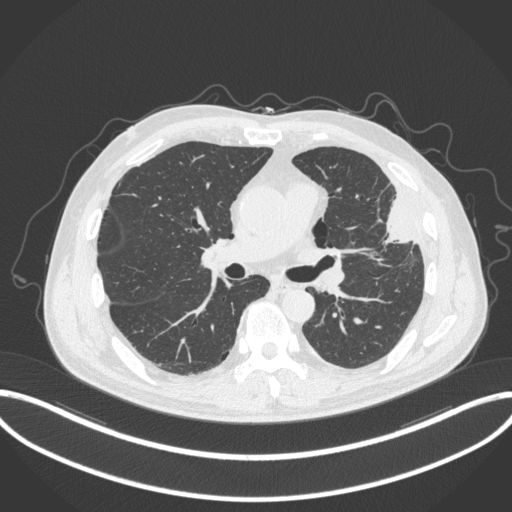
Chest CT, one axial slice. Slice 189 of 382 in the series (ordered by position). Reconstruction kernel B31f. 120 kVp. Lung window (W 1500 / L -600 HU). 1 mm slice thickness. 512 × 512 image matrix, field of view 415 × 415 mm. Male patient, age 64 years. Case-level facts recorded for this patient, not image findings: clinical TNM (as recorded): T4 N1 M0; histopathological grade: G3.
Structures marked on this image (bounding box drawn by a radiologist):
- lung tumour (recorded histology: adenocarcinoma): bounding box <373,190,419,250> (left, top, right, bottom; pixels)